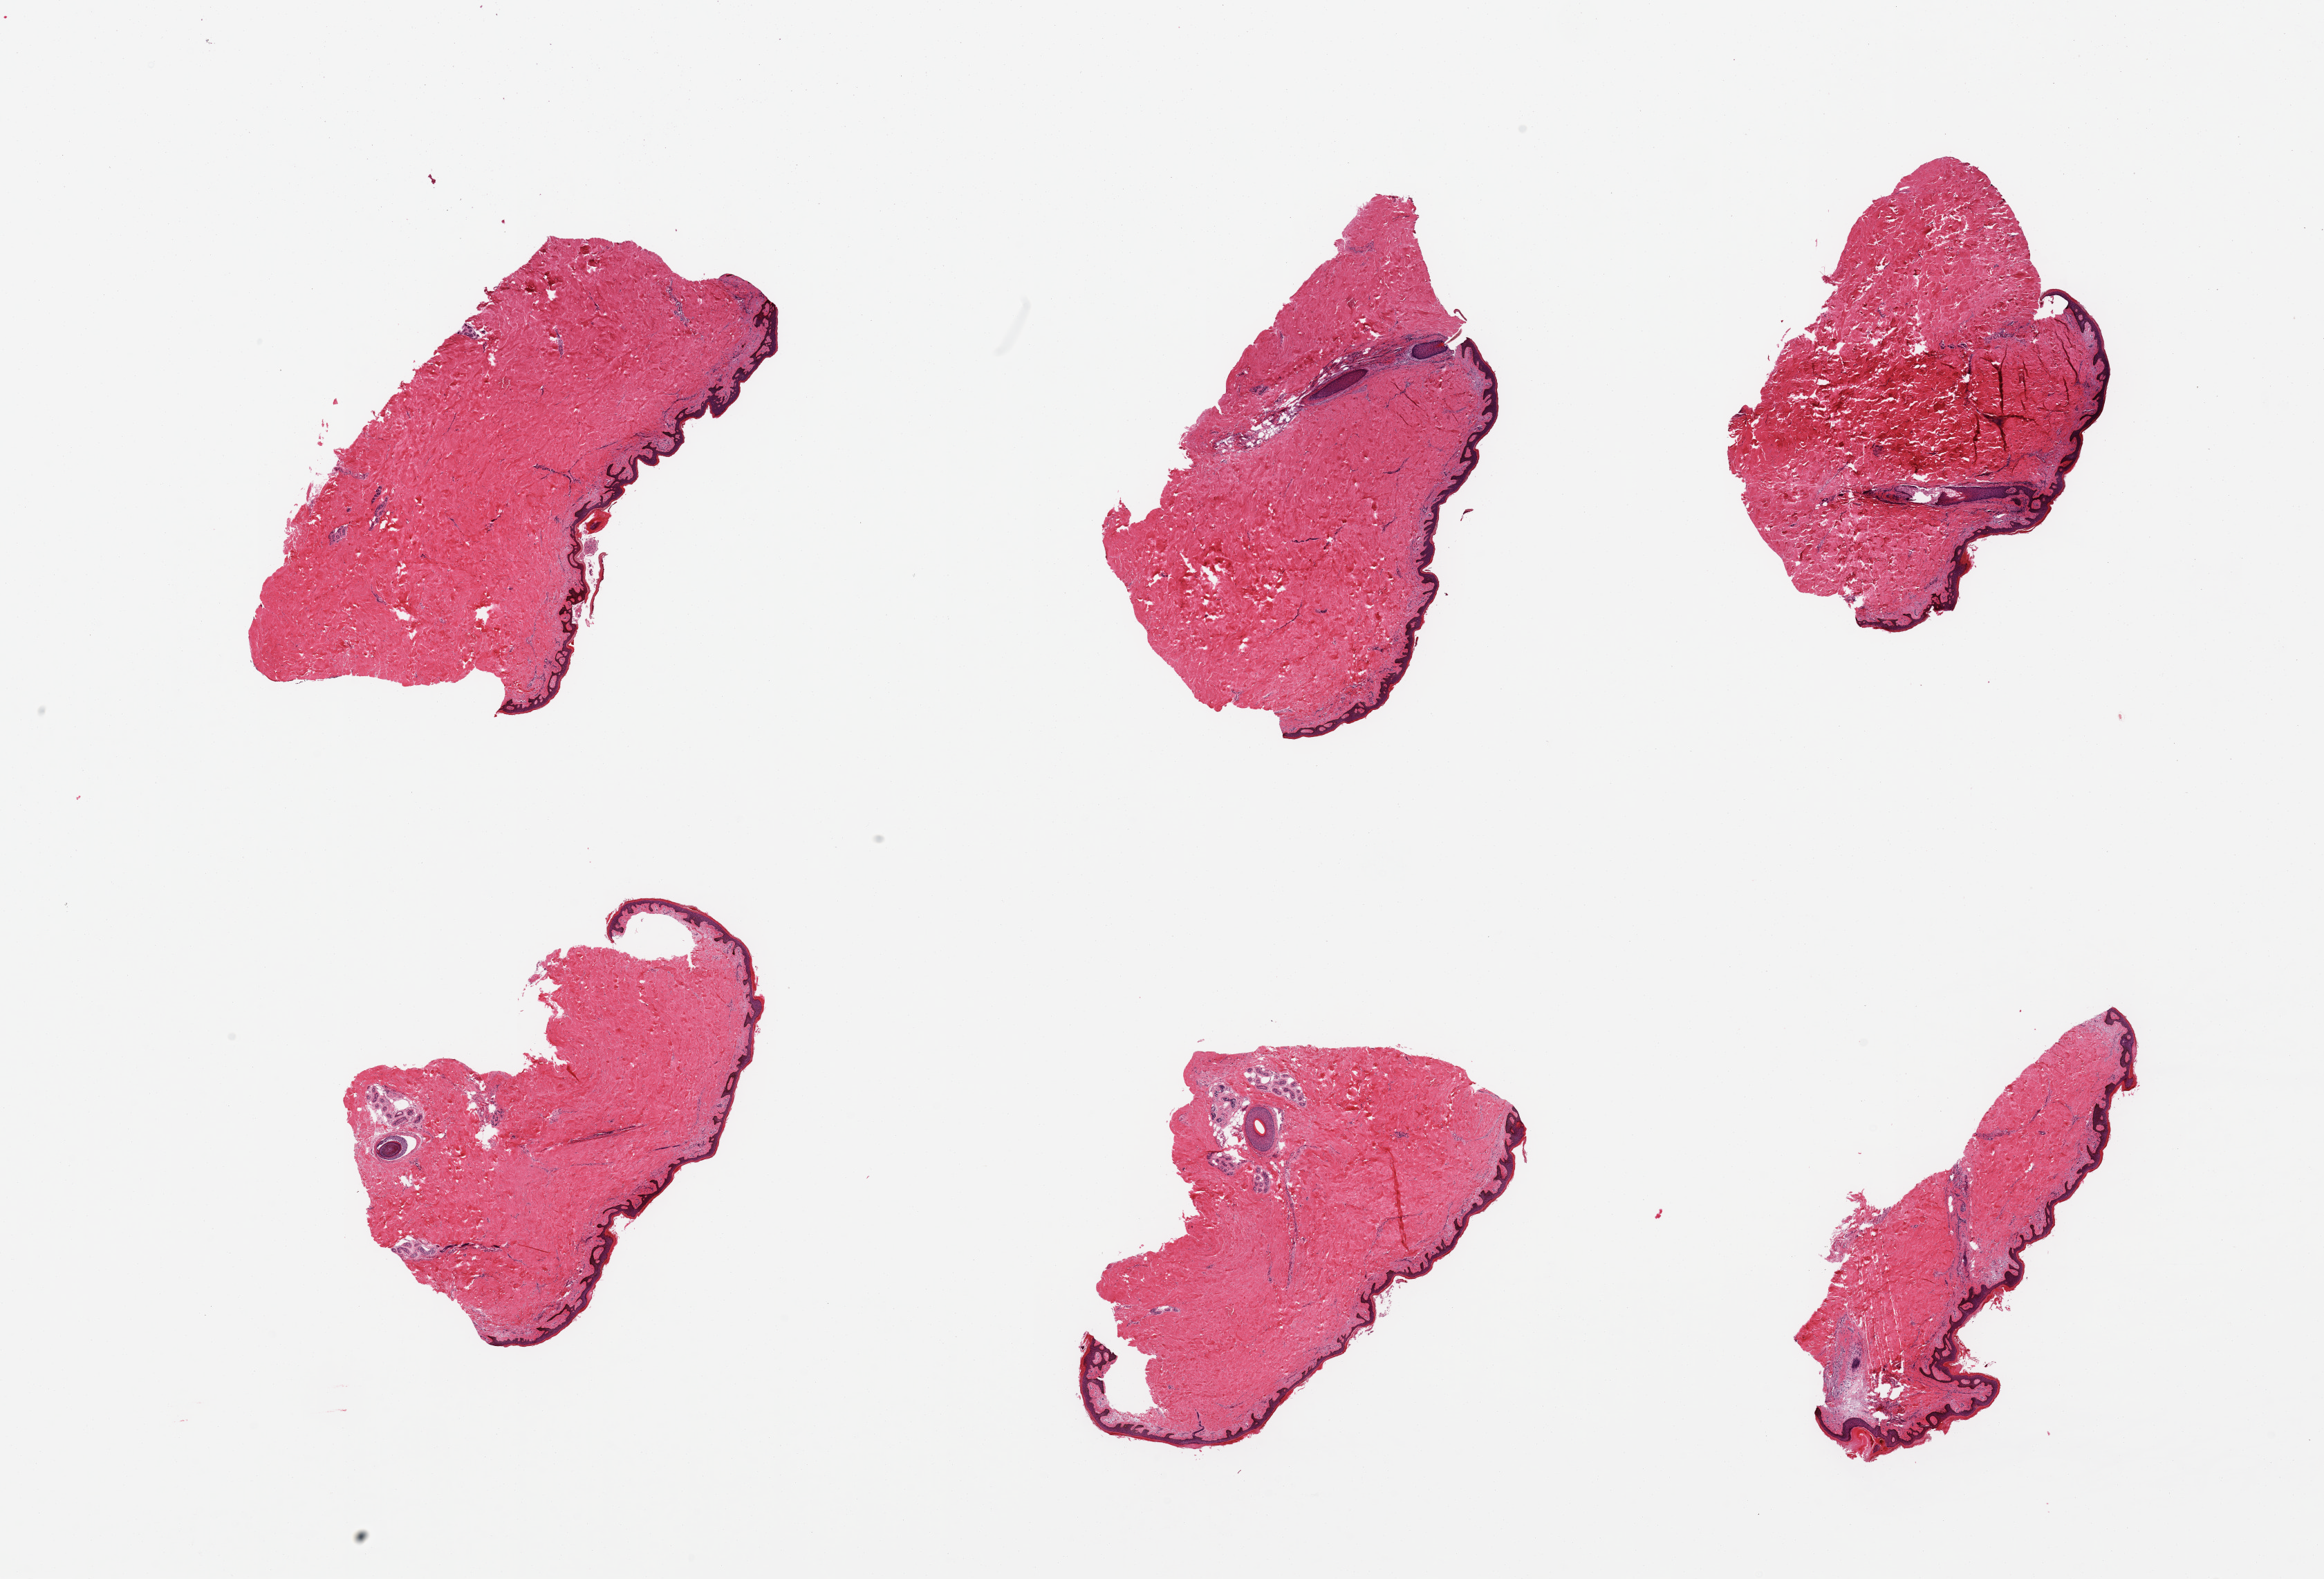
Digitized H&E-stained section, whole scanned area (about 26.6 x 18.1 mm) shown as a low-resolution overview. PAXgene-fixed, paraffin-embedded tissue. Section of skin of suprapubic region (target tissue). Tissue donor sample. Male donor.
• review note (as recorded): 6 pieces, no dermal fat, squamous epithelium is ~35-45 microns